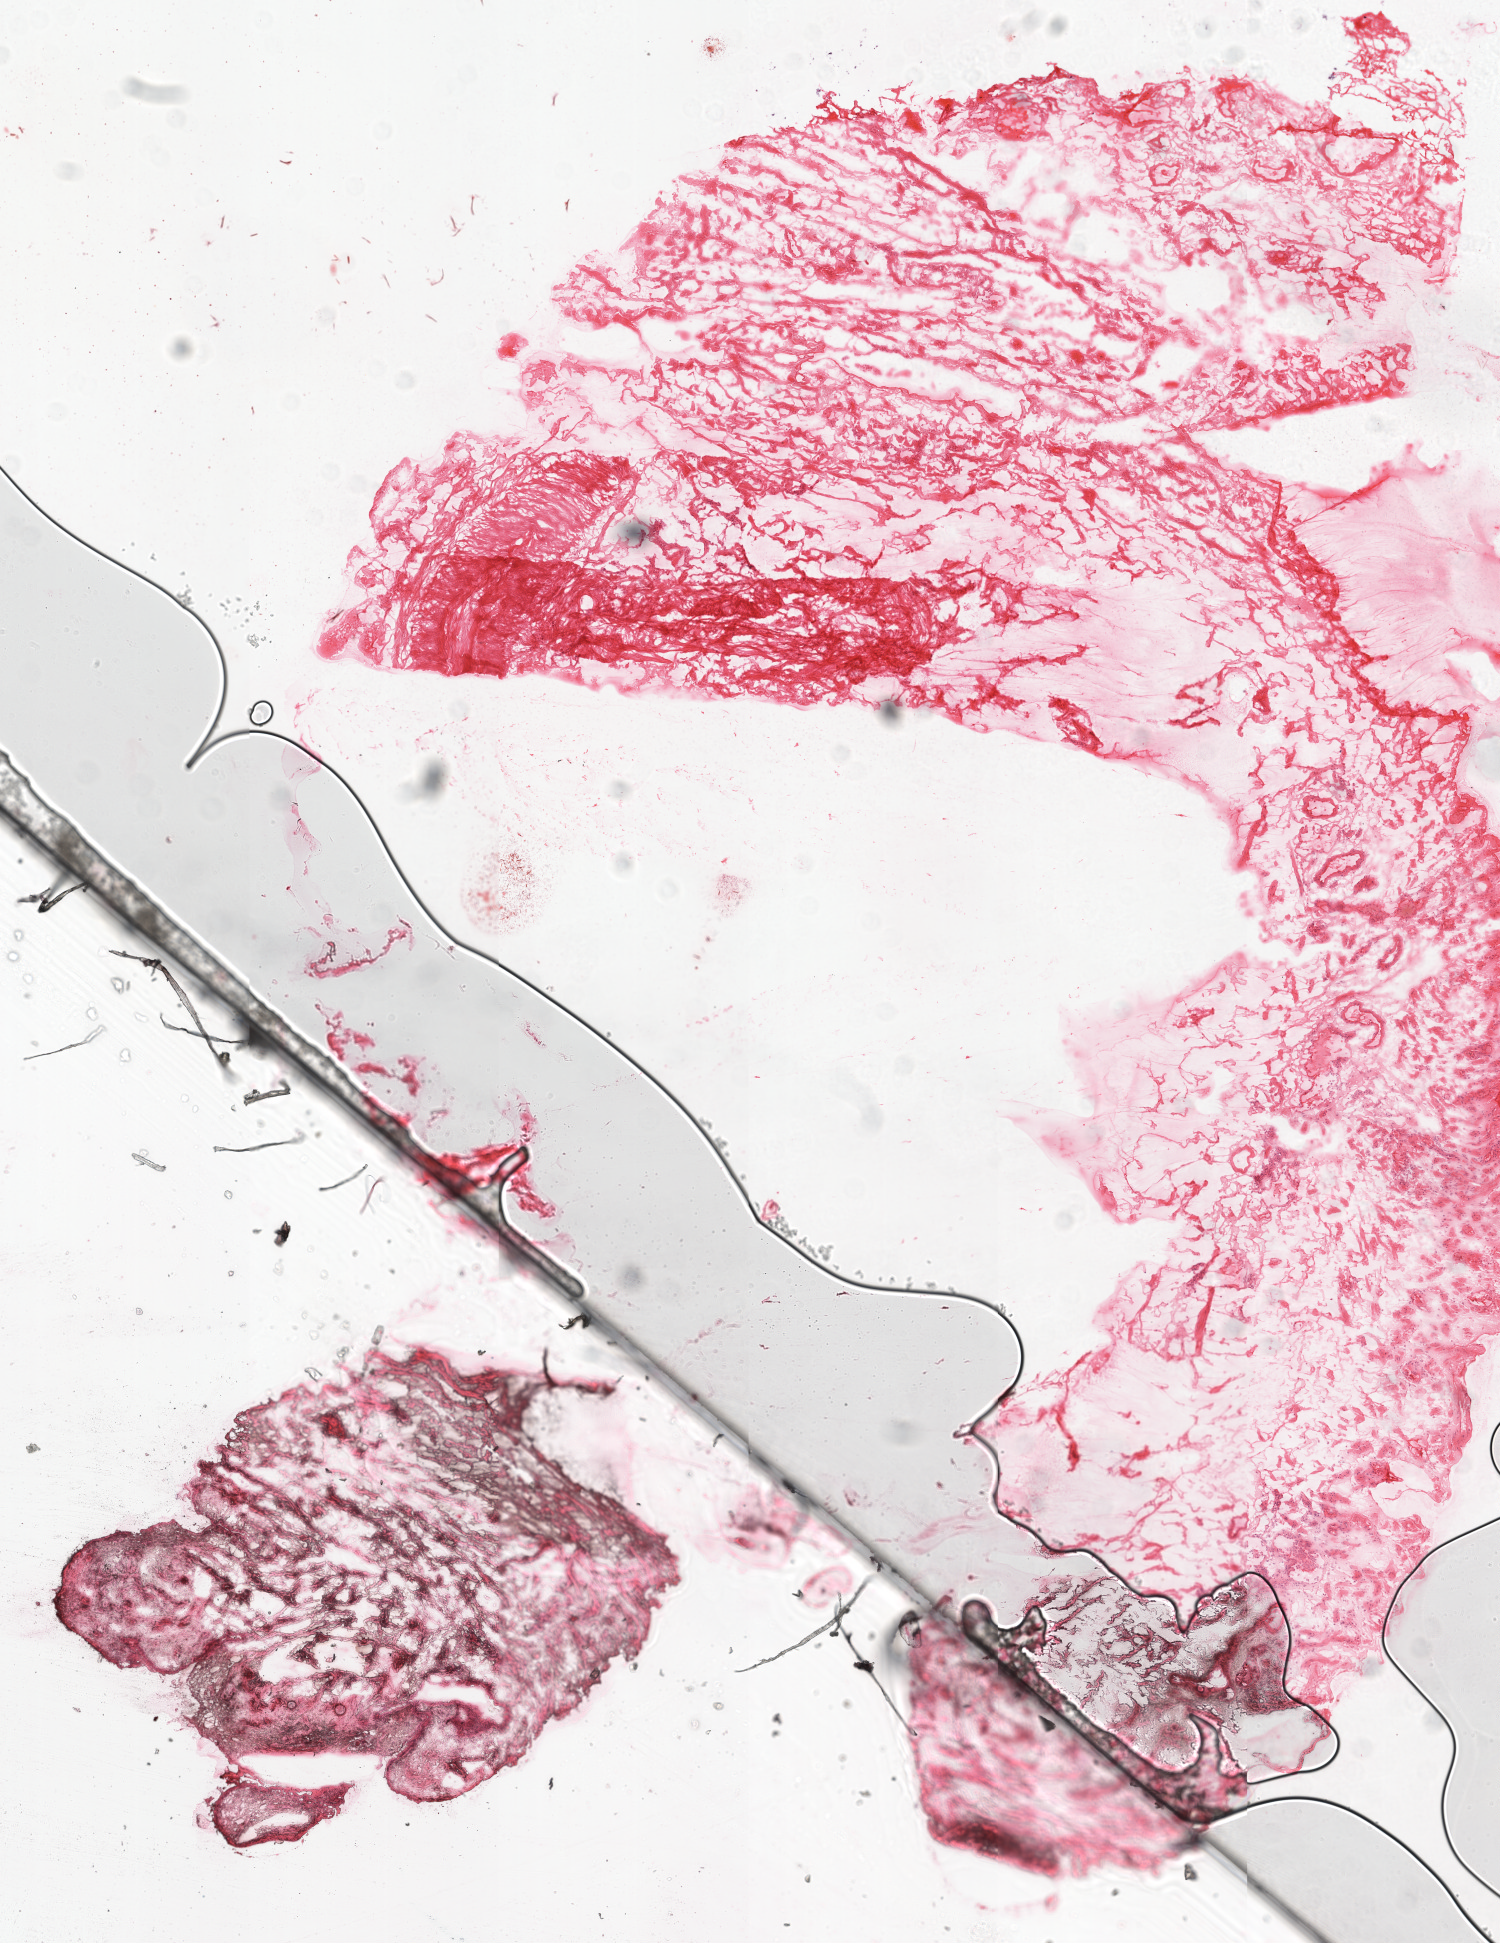
H&E-stained whole-slide image, shown as a low-resolution overview of the whole scanned area (about 6.0 x 7.8 mm); frozen section from the top of the tissue portion; solid tissue normal (non-tumour tissue) sample from the ovary. Patient: female, age at initial diagnosis 42 years.
This section: solid tissue normal (non-tumour) sample from the same patient. Patient diagnosis: Serous cystadenocarcinoma, NOS.